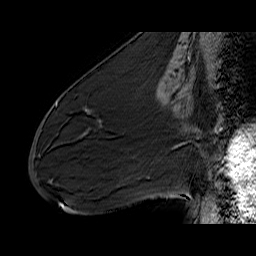
Breast MRI (dynamic contrast-enhanced), one sagittal slice. Position 28 of 60 along the scan axis. Dynamic contrast-enhanced series, time point 2 of 6 at this slice position (early post-contrast). 1.5 T. TE 6.5 ms, TR 32.9 ms. 4 mm slice thickness. 256 × 256 image matrix, field of view 200 × 200 mm. Female patient. Case-level facts recorded for this patient, not image findings: setting: breast cancer imaged before/during neoadjuvant chemotherapy; receptor status: HER2-positive.
Annotated regions visible in this slice (semi-automatic segmentation, software-assisted and operator-edited):
- analysis volume of interest (the breast-tissue region the enhancement analysis was run in; not a lesion): bounding box (x1, y1, x2, y2) in pixels: (72, 88, 133, 137)
- tumour enhancement mask (voxels above the 100 % enhancement threshold inside the analysis volume of interest): (89, 121, 102, 130)